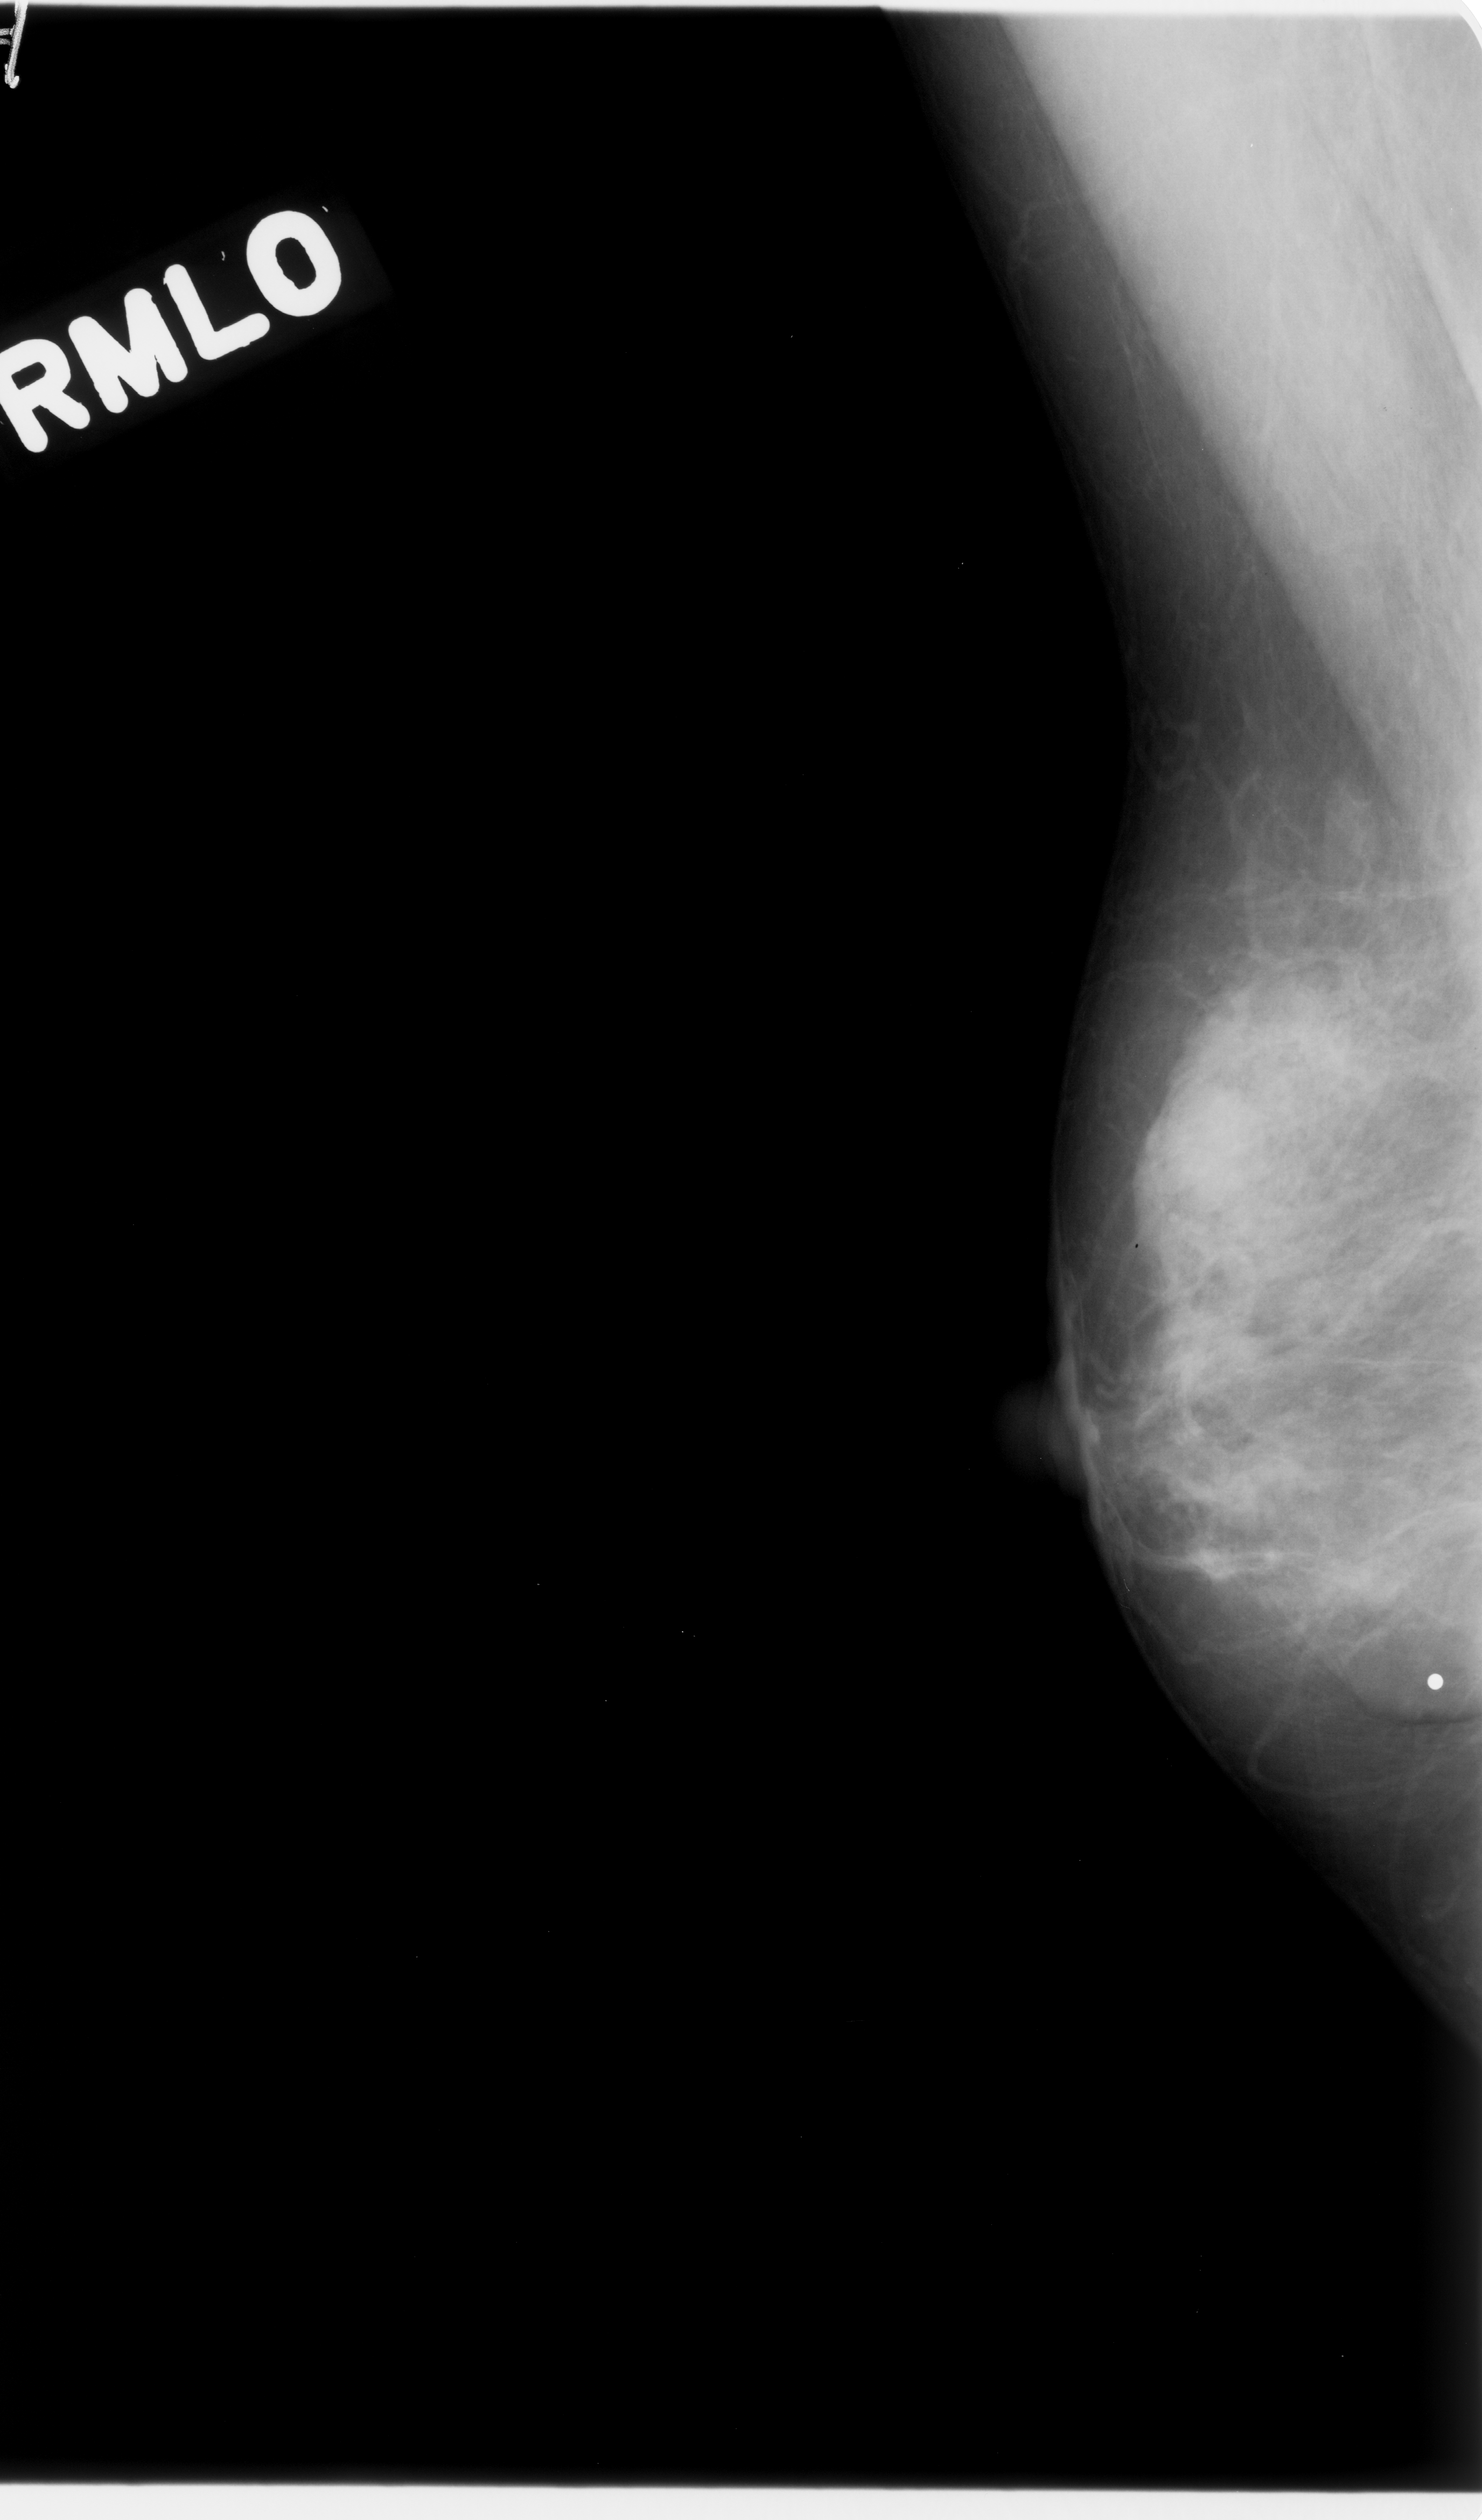
Digitized screen-film mammogram; right breast; MLO view; breast composition: heterogeneously dense (BI-RADS density category 3 of 4); 1482 × 2520 image matrix.
Expert-marked regions of interest on this film, with their recorded descriptors:
- mass, shape lobulated, margins microlobulated; BI-RADS assessment category 4; pathology (as recorded): benign: bounding box [x1, y1, x2, y2] px = [1154, 1055, 1310, 1218]